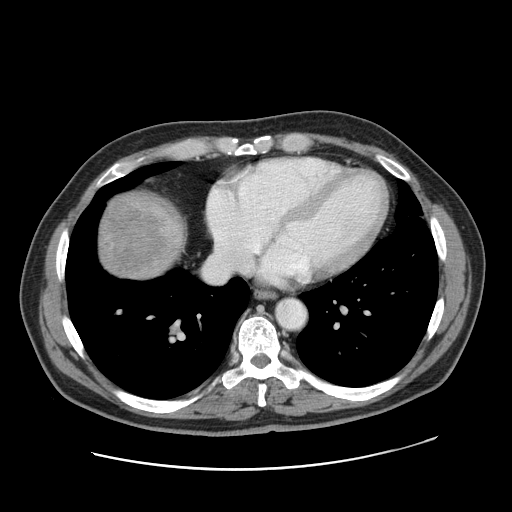
Contrast-enhanced abdominal CT, one axial slice; position 159 of 178 along the scan axis; 120 kVp; intravenous contrast given; soft-tissue window (W 400 / L 40 HU); 512 × 512 image matrix, field of view 403 × 403 mm. Male patient, age 63 years. From the clinical record (not read from this slice): diagnosis: colorectal cancer liver metastases, imaged before liver resection; multiple liver metastases: yes.
Structures marked on this image (expert manual segmentation):
- liver: bounding box [x1, y1, x2, y2] px = [97, 194, 186, 280]
- liver metastasis: [99, 195, 165, 277]